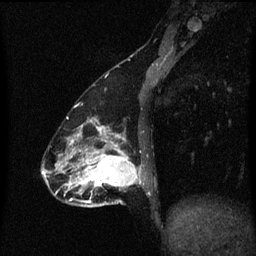
Breast MRI (dynamic contrast-enhanced), one sagittal slice; slice 20 of 60 in the series (ordered by position); dynamic contrast-enhanced series, image 2 of 3 at this slice position (ordered by acquisition); 1.5 T; TE 4.2 ms, TR 8.4 ms; 2 mm slice thickness; 256 × 256 image matrix, field of view 200 × 200 mm. Patient: female, 47 years.
Structures marked on this image (semi-automatic segmentation, software-assisted and operator-edited):
- analysis volume of interest (the breast-tissue region the enhancement analysis was run in; not a lesion): bounding box <81,138,146,207> (left, top, right, bottom; pixels)
- tumour enhancement mask (voxels above the 70 % enhancement threshold inside the analysis volume of interest): <81,138,141,203>